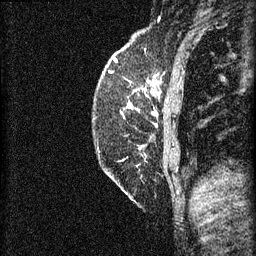
Breast MRI (dynamic contrast-enhanced), one sagittal slice; position 17 of 60 along the scan axis; 3 images stored at this slice position (order not interpretable as contrast timing); 1.5 T; TE 4.2 ms, TR 8.2 ms; 2 mm slice thickness; 256 × 256 image matrix, field of view 180 × 180 mm. Patient: female, 59 years.
Outlined on this slice (semi-automatic segmentation, software-assisted and operator-edited):
- analysis volume of interest (the breast-tissue region the enhancement analysis was run in; not a lesion): bounding box (x1, y1, x2, y2) in pixels: (99, 76, 155, 119)
- tumour enhancement mask (voxels above the 70 % enhancement threshold inside the analysis volume of interest): (128, 92, 155, 109)